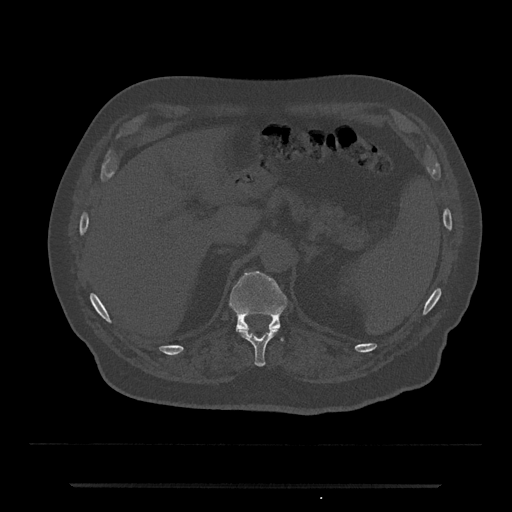
CT including the spine, one axial slice; slice 621 of 797 in the series (ordered by position); reconstruction kernel Br40s/3; bone window (W 1800 / L 400 HU); 0.5 mm slice thickness; 512 × 512 image matrix, field of view 434 × 434 mm. Patient: male, 80 years. Case-level facts recorded for this patient, not image findings: primary cancer: prostate; vertebrae with lytic lesions (as recorded): L1, T11.
Structures marked on this image (semi-automatic segmentation, software-assisted and operator-edited):
- T11 vertebra: box from (x=238, y=329) to (x=278, y=367) px
- T12 vertebra: (x=229, y=270)–(x=288, y=342)